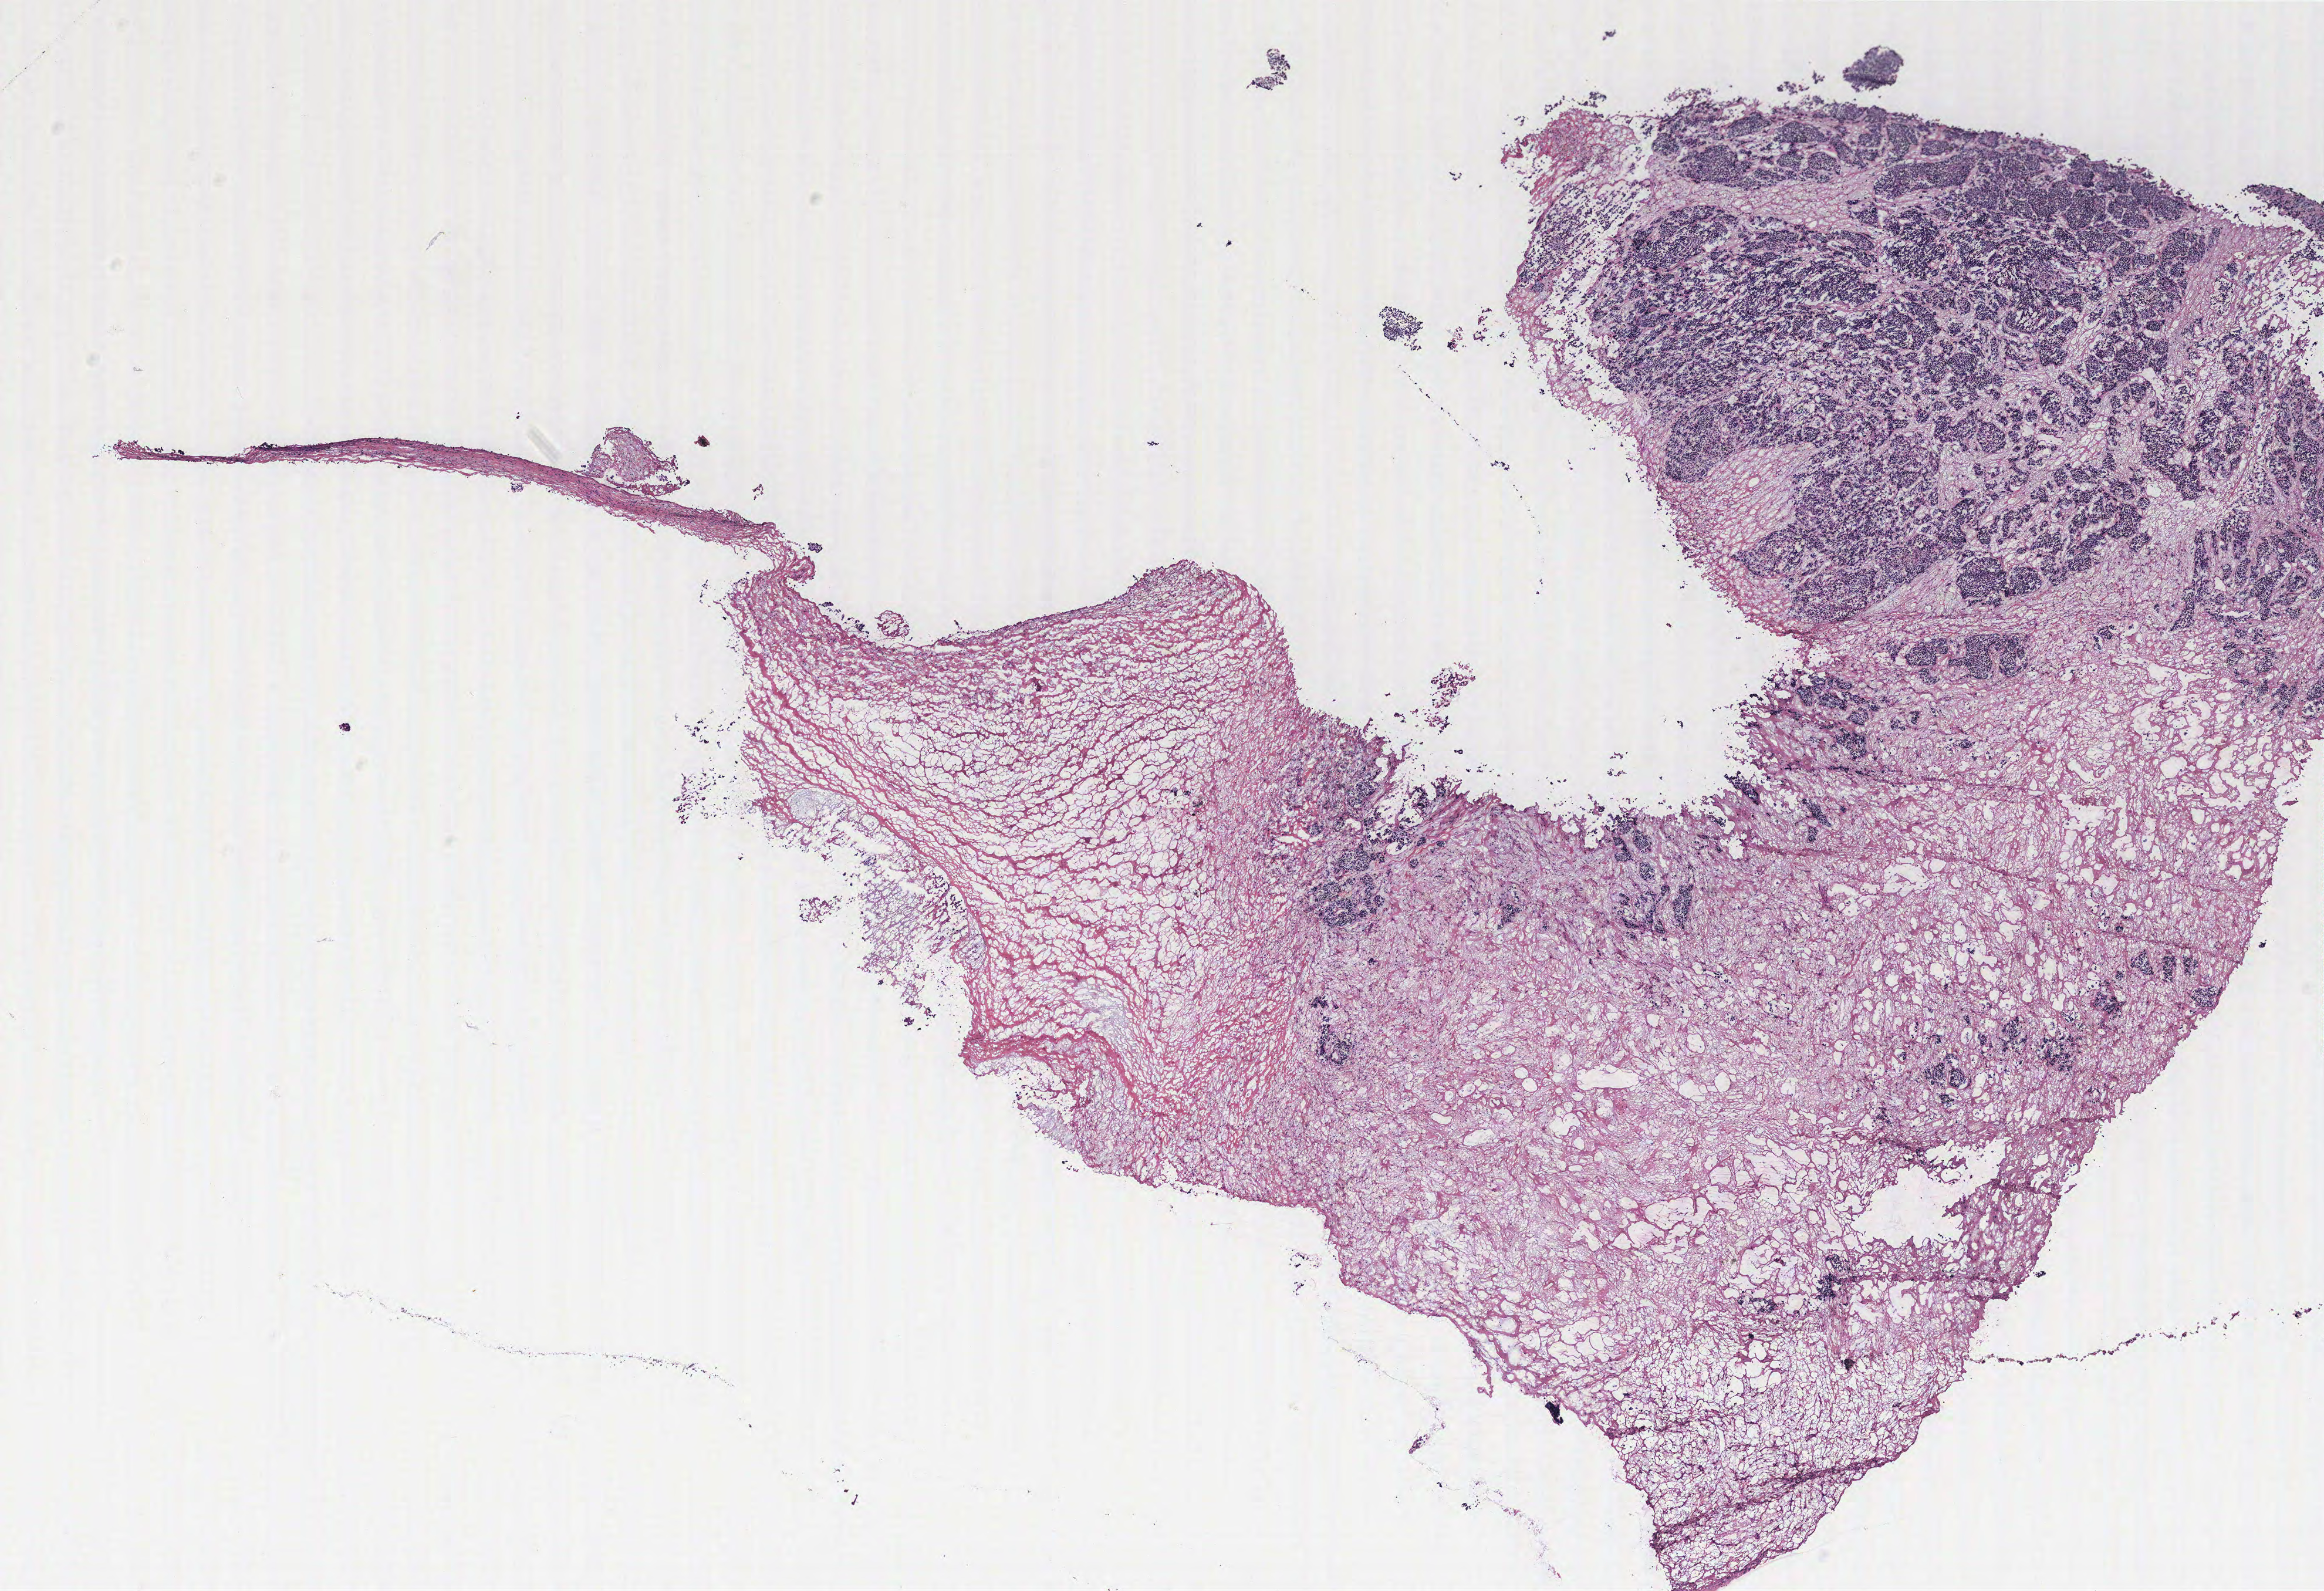
Hematoxylin and eosin (H&E) stained whole-slide image, low-resolution overview of the scanned area, about 15.8 x 10.8 mm (from a 40x scan); ovary, tumour tissue. 57-year-old female patient.
Diagnosis: Serous adenocarcinoma, NOS. Primary tumour site (as recorded): ovary.